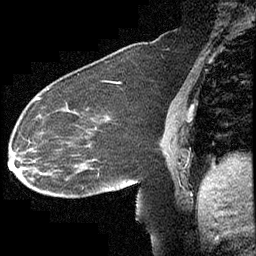
Breast MRI (dynamic contrast-enhanced), one sagittal slice; slice 156 of 232 in the series (ordered by position); dynamic contrast-enhanced study with each time point stored as its own series, time point 2 of 4 at this slice position (early post-contrast, ordered by acquisition time); 1.5 T; TE 4.2 ms, TR 6.7 ms; 256 × 256 image matrix, field of view 200 × 200 mm. Female patient, age 63 years. From the clinical record (not read from this slice): setting: breast cancer imaged before/during neoadjuvant chemotherapy; receptor status: triple-negative.
Structures marked on this image (semi-automatic segmentation, software-assisted and operator-edited):
- analysis volume of interest (the breast-tissue region the enhancement analysis was run in; not a lesion): bounding box [x1, y1, x2, y2] px = [13, 90, 140, 211]
- tumour enhancement mask (voxels above the 70 % enhancement threshold inside the analysis volume of interest): [18, 97, 40, 169]